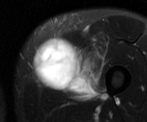
MRI of an extremity soft-tissue mass, one axial slice; slice 16 of 52 in the series (ordered by position); T2-weighted fat-saturated; MR volume resampled by the dataset authors to the PET/CT grid (not the native acquisition matrix); 147 × 122 image matrix. Male patient. Case-level facts recorded for this patient, not image findings: histological type: pleiomorphic liposarcoma; grade: high; site of the primary tumour: left thigh.
Annotated regions visible in this slice (expert contour drawn on MRI and transferred to this co-registered scan by the dataset authors):
- gross tumour volume including surrounding oedema: box from (x=34, y=34) to (x=101, y=99) px
- gross tumour volume (mass): (x=34, y=35)–(x=83, y=90)